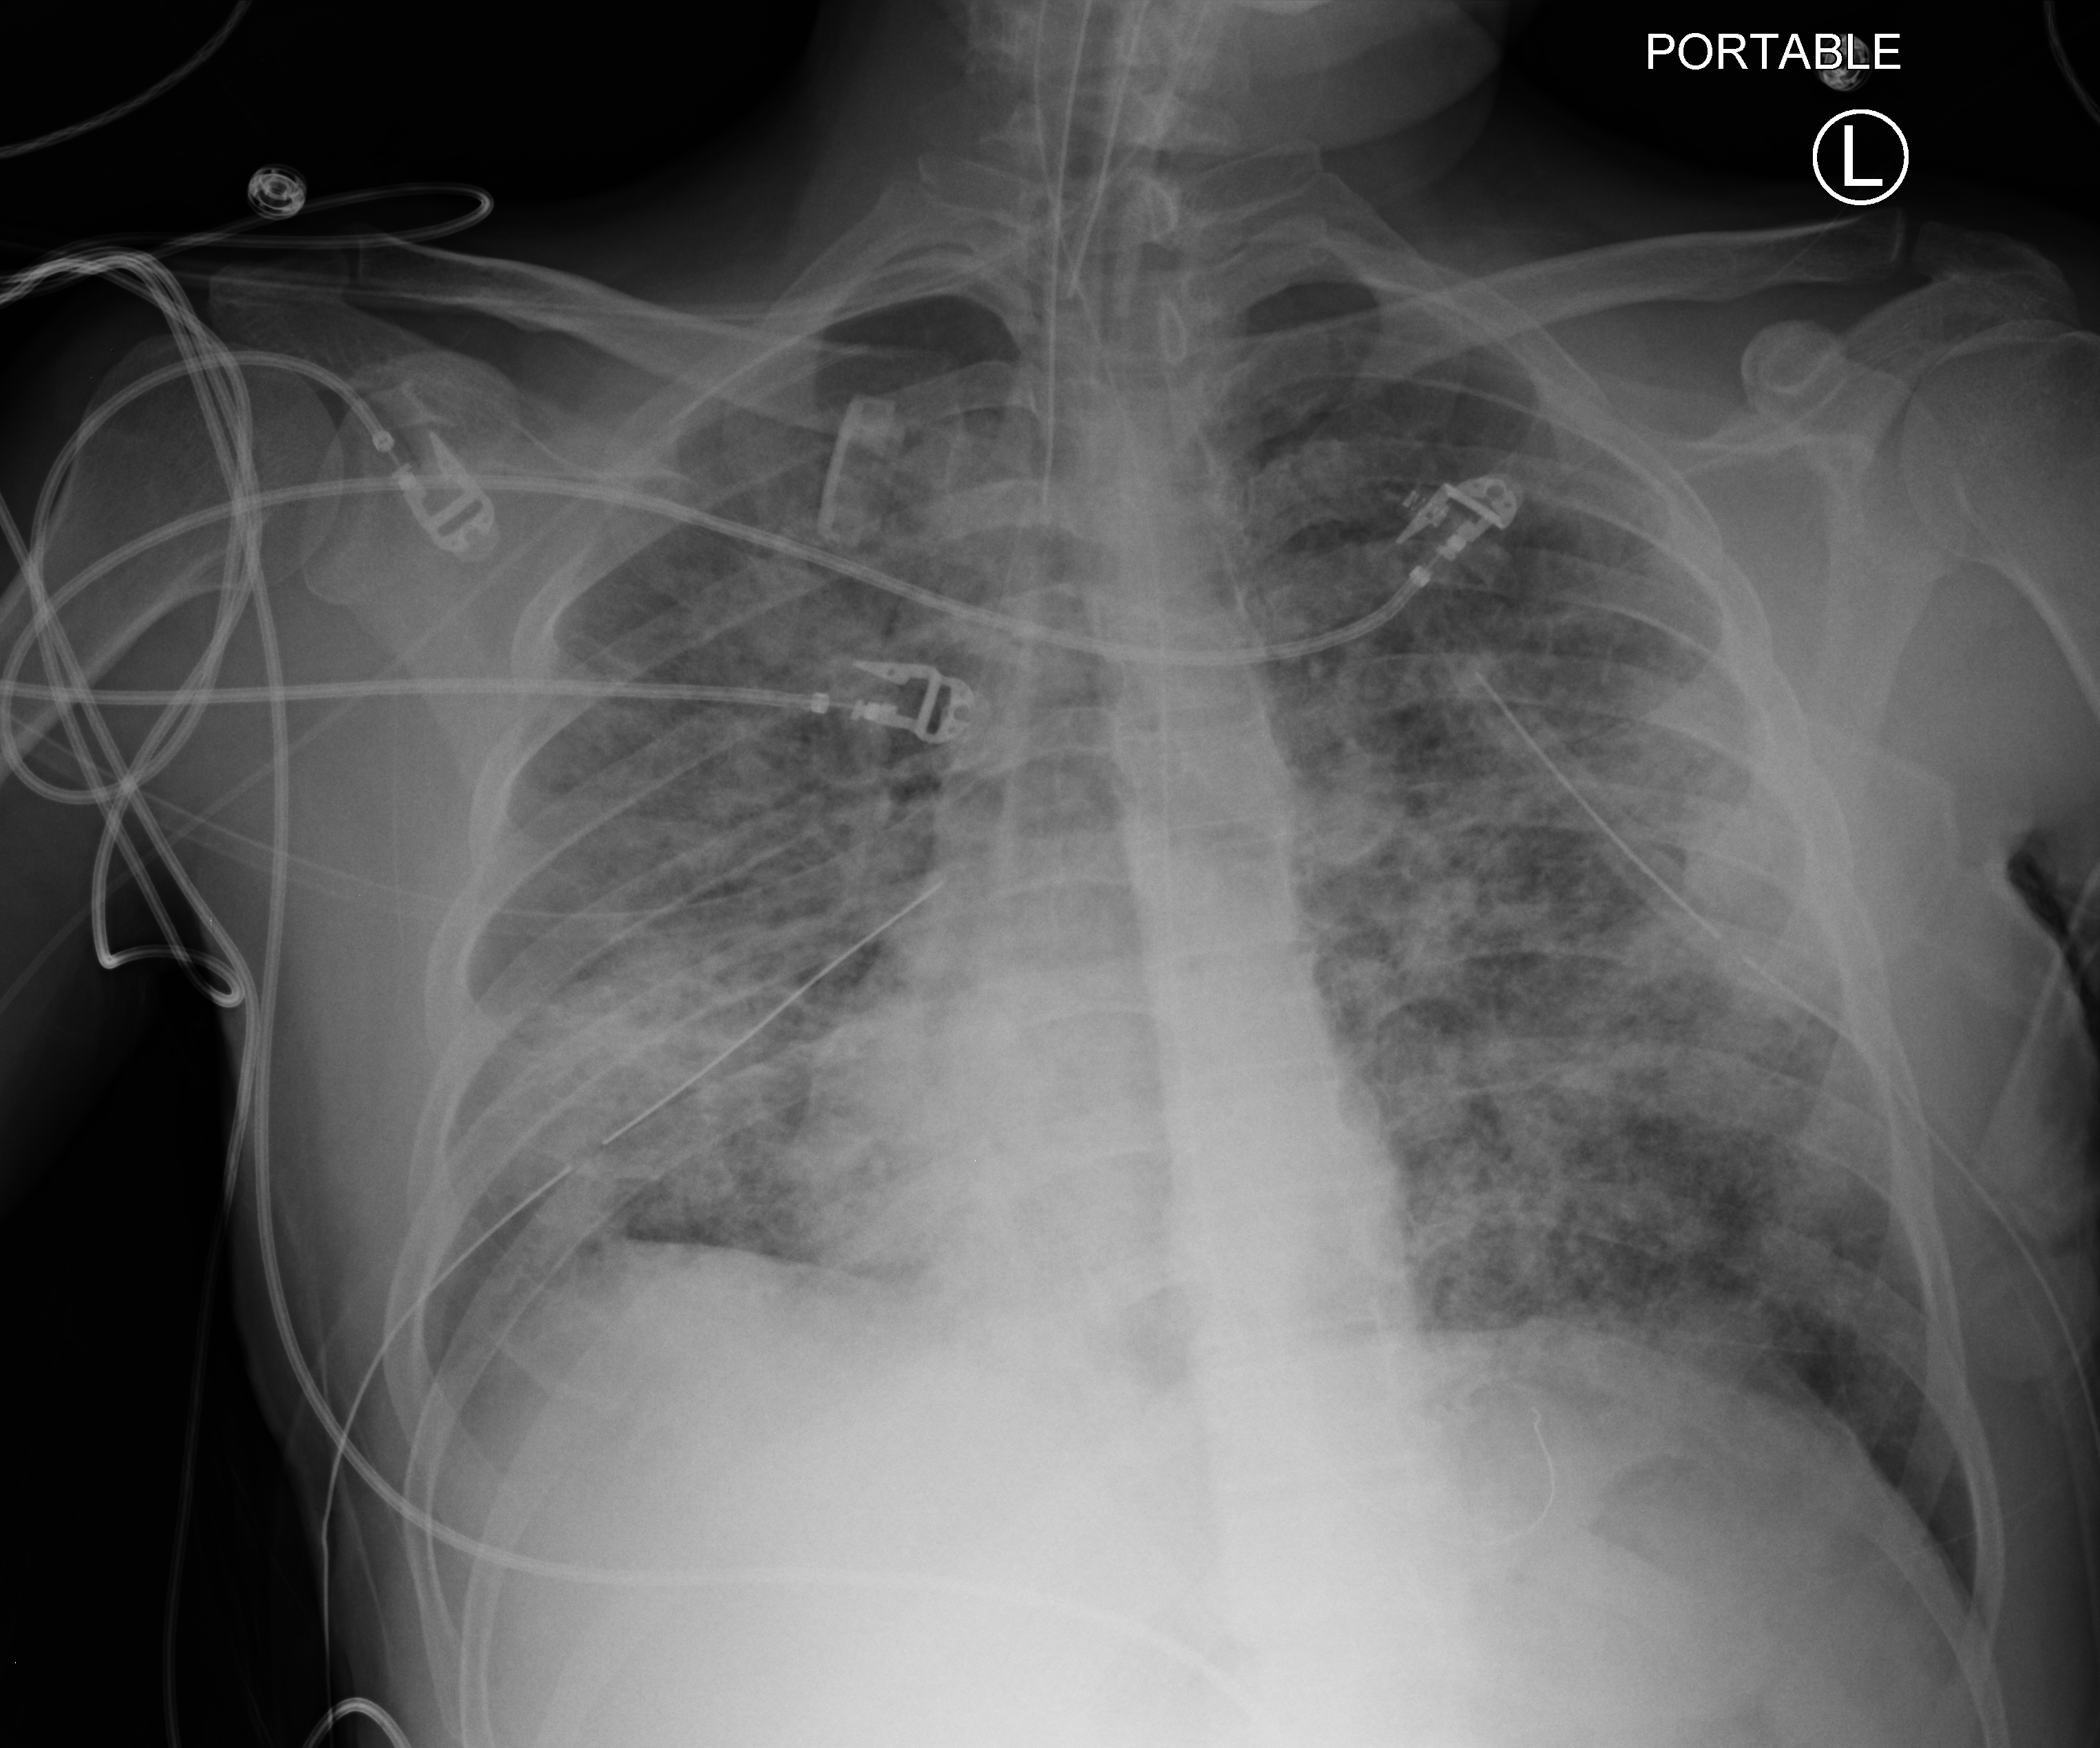
Bedside chest radiograph (computed radiography). Male patient hospitalised with COVID-19, age 18–59 years.
Admission-level facts for this patient (not findings on this image; timing relative to this image not recorded):
- other chronic lung disease (admission record): no
- admitted to intensive care during this hospital stay: yes
- mechanically ventilated during this hospital stay: yes